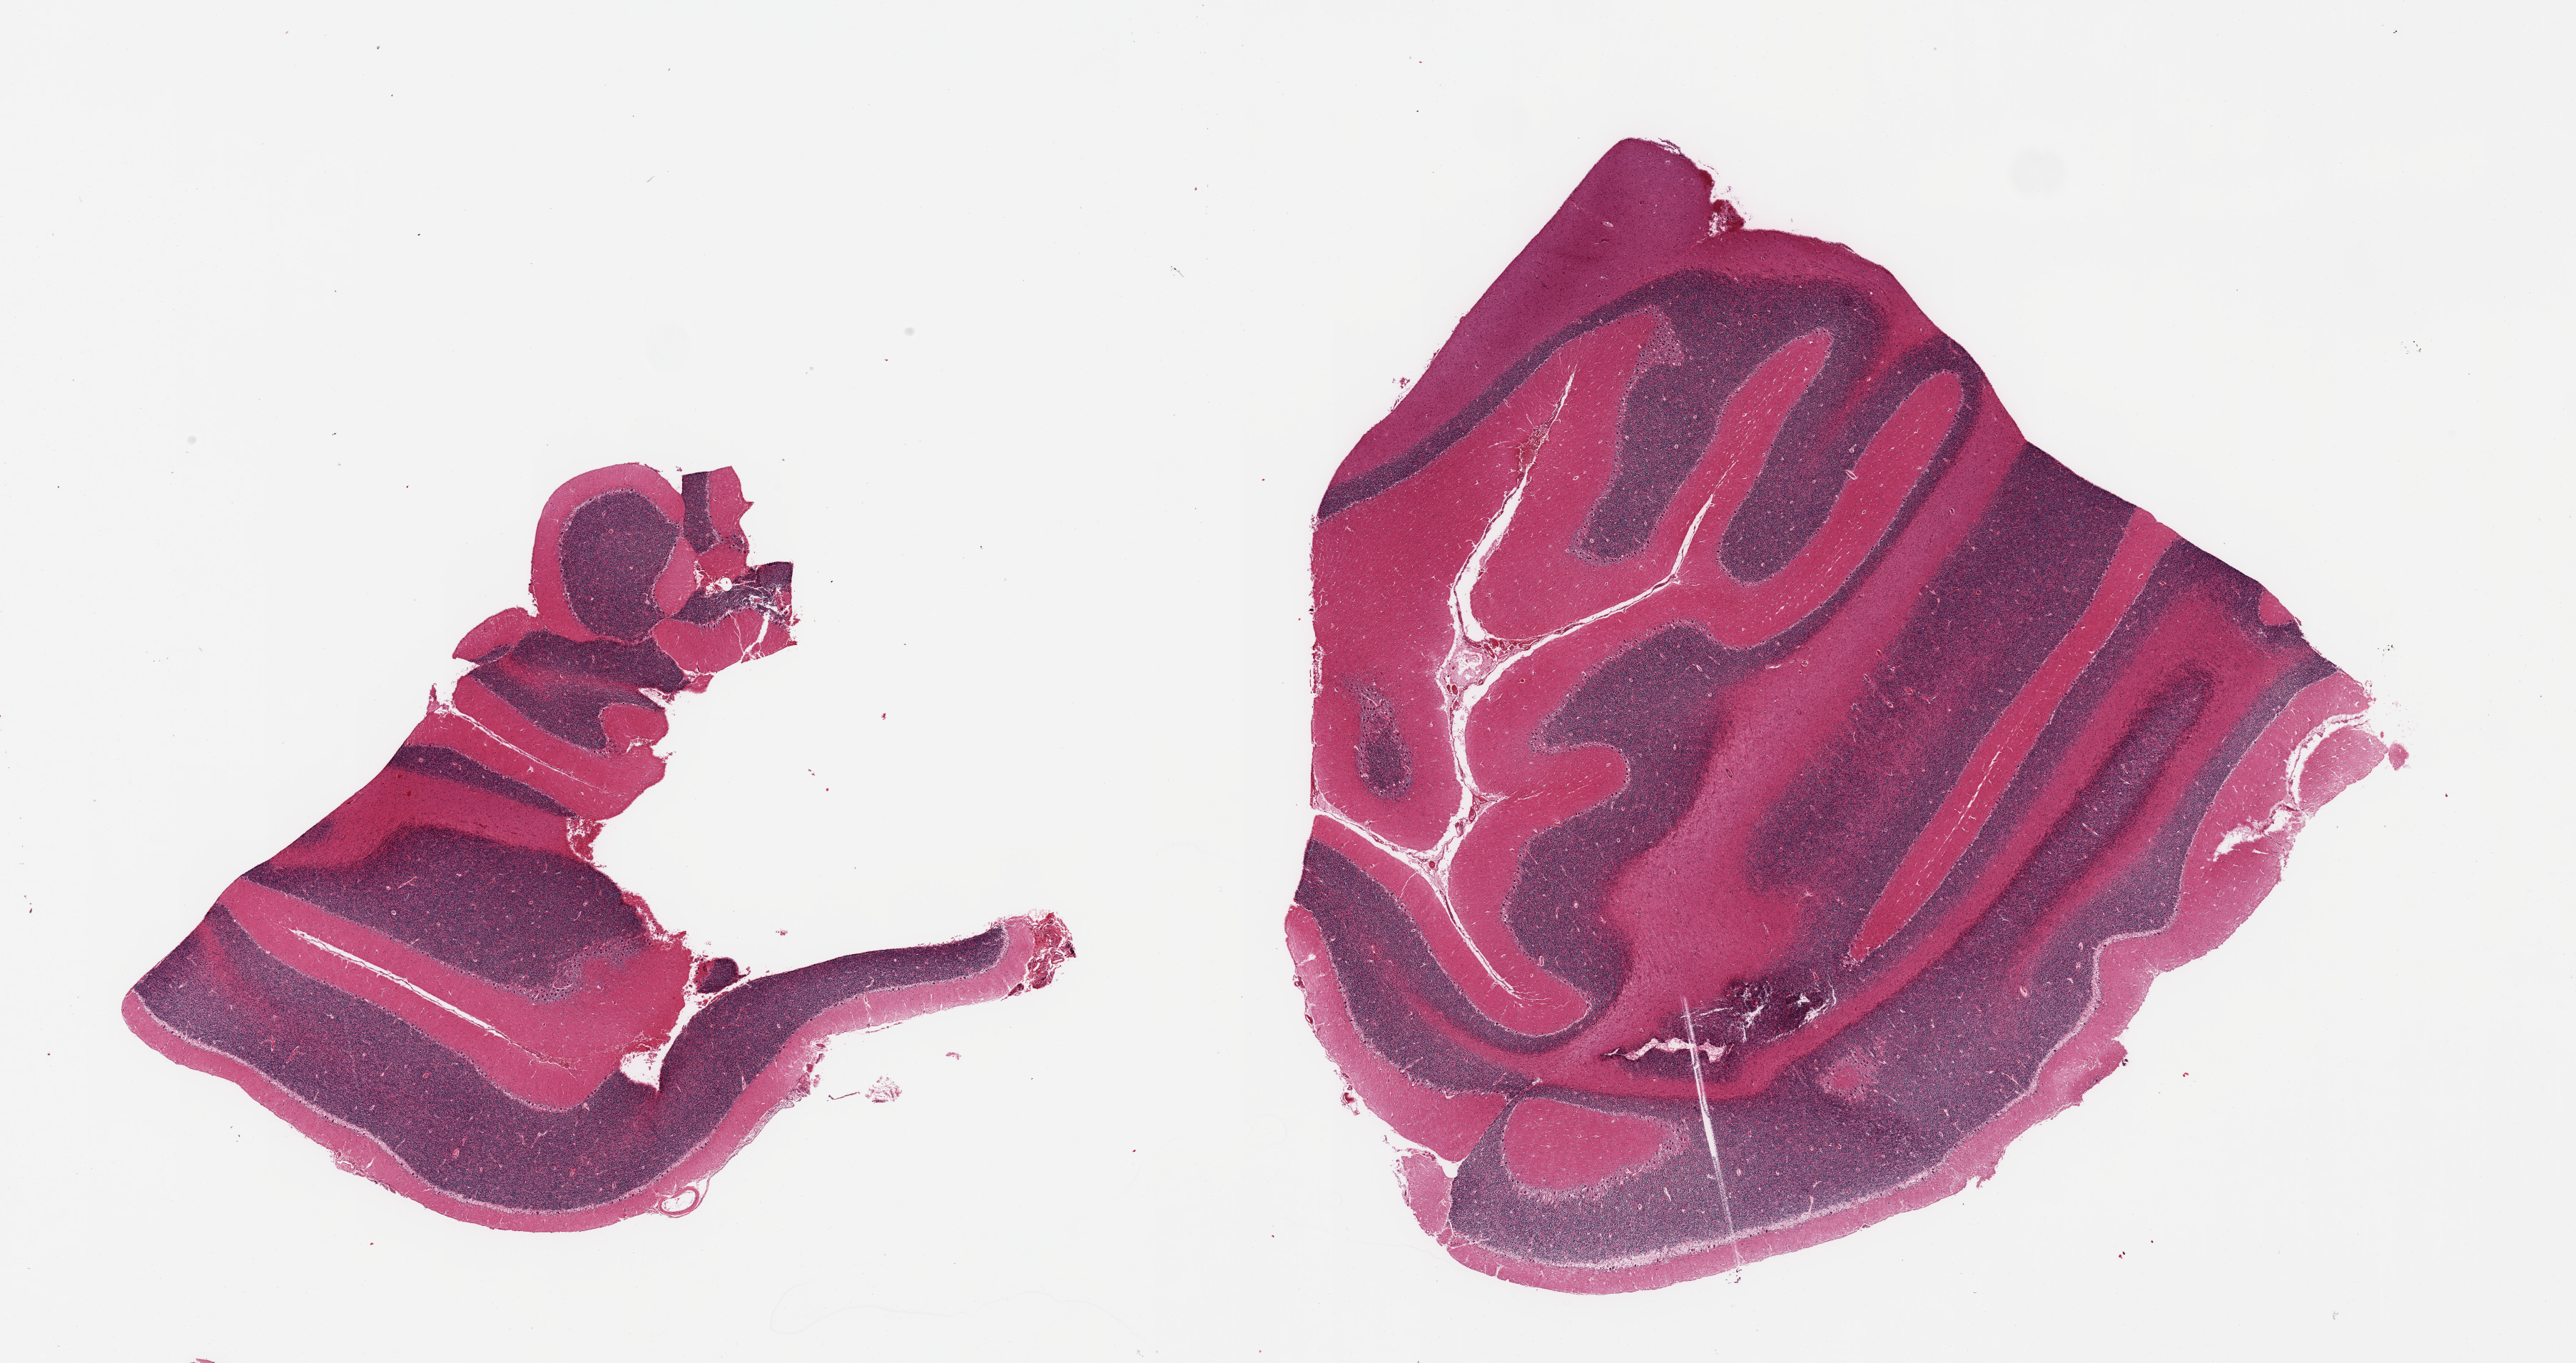
Haematoxylin and eosin whole-slide image, whole scanned area (about 28.5 x 15.1 mm, slide scanned at 20x) shown as a low-resolution overview. PAXgene-fixed paraffin-embedded (PFPE) section. Sampled site (target tissue): cerebellum. Tissue donor sample. Donor: male.
- review note (as recorded): 2 pieces, no abnormalities